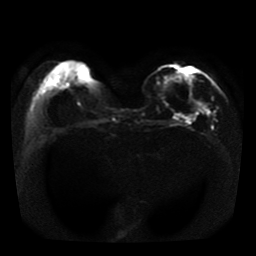
Breast MRI, one axial slice. Slice 12 of 41 in the series (ordered by position). Diffusion-weighted series; image 2 of 4 stored at this slice position (different b-values; order by instance number). 1.5 T. 256 × 256 image matrix, field of view 330 × 330 mm. Female patient.
Outlined on this slice (expert manual segmentation):
- tumour on diffusion-weighted imaging: box from (x=182, y=101) to (x=204, y=117) px